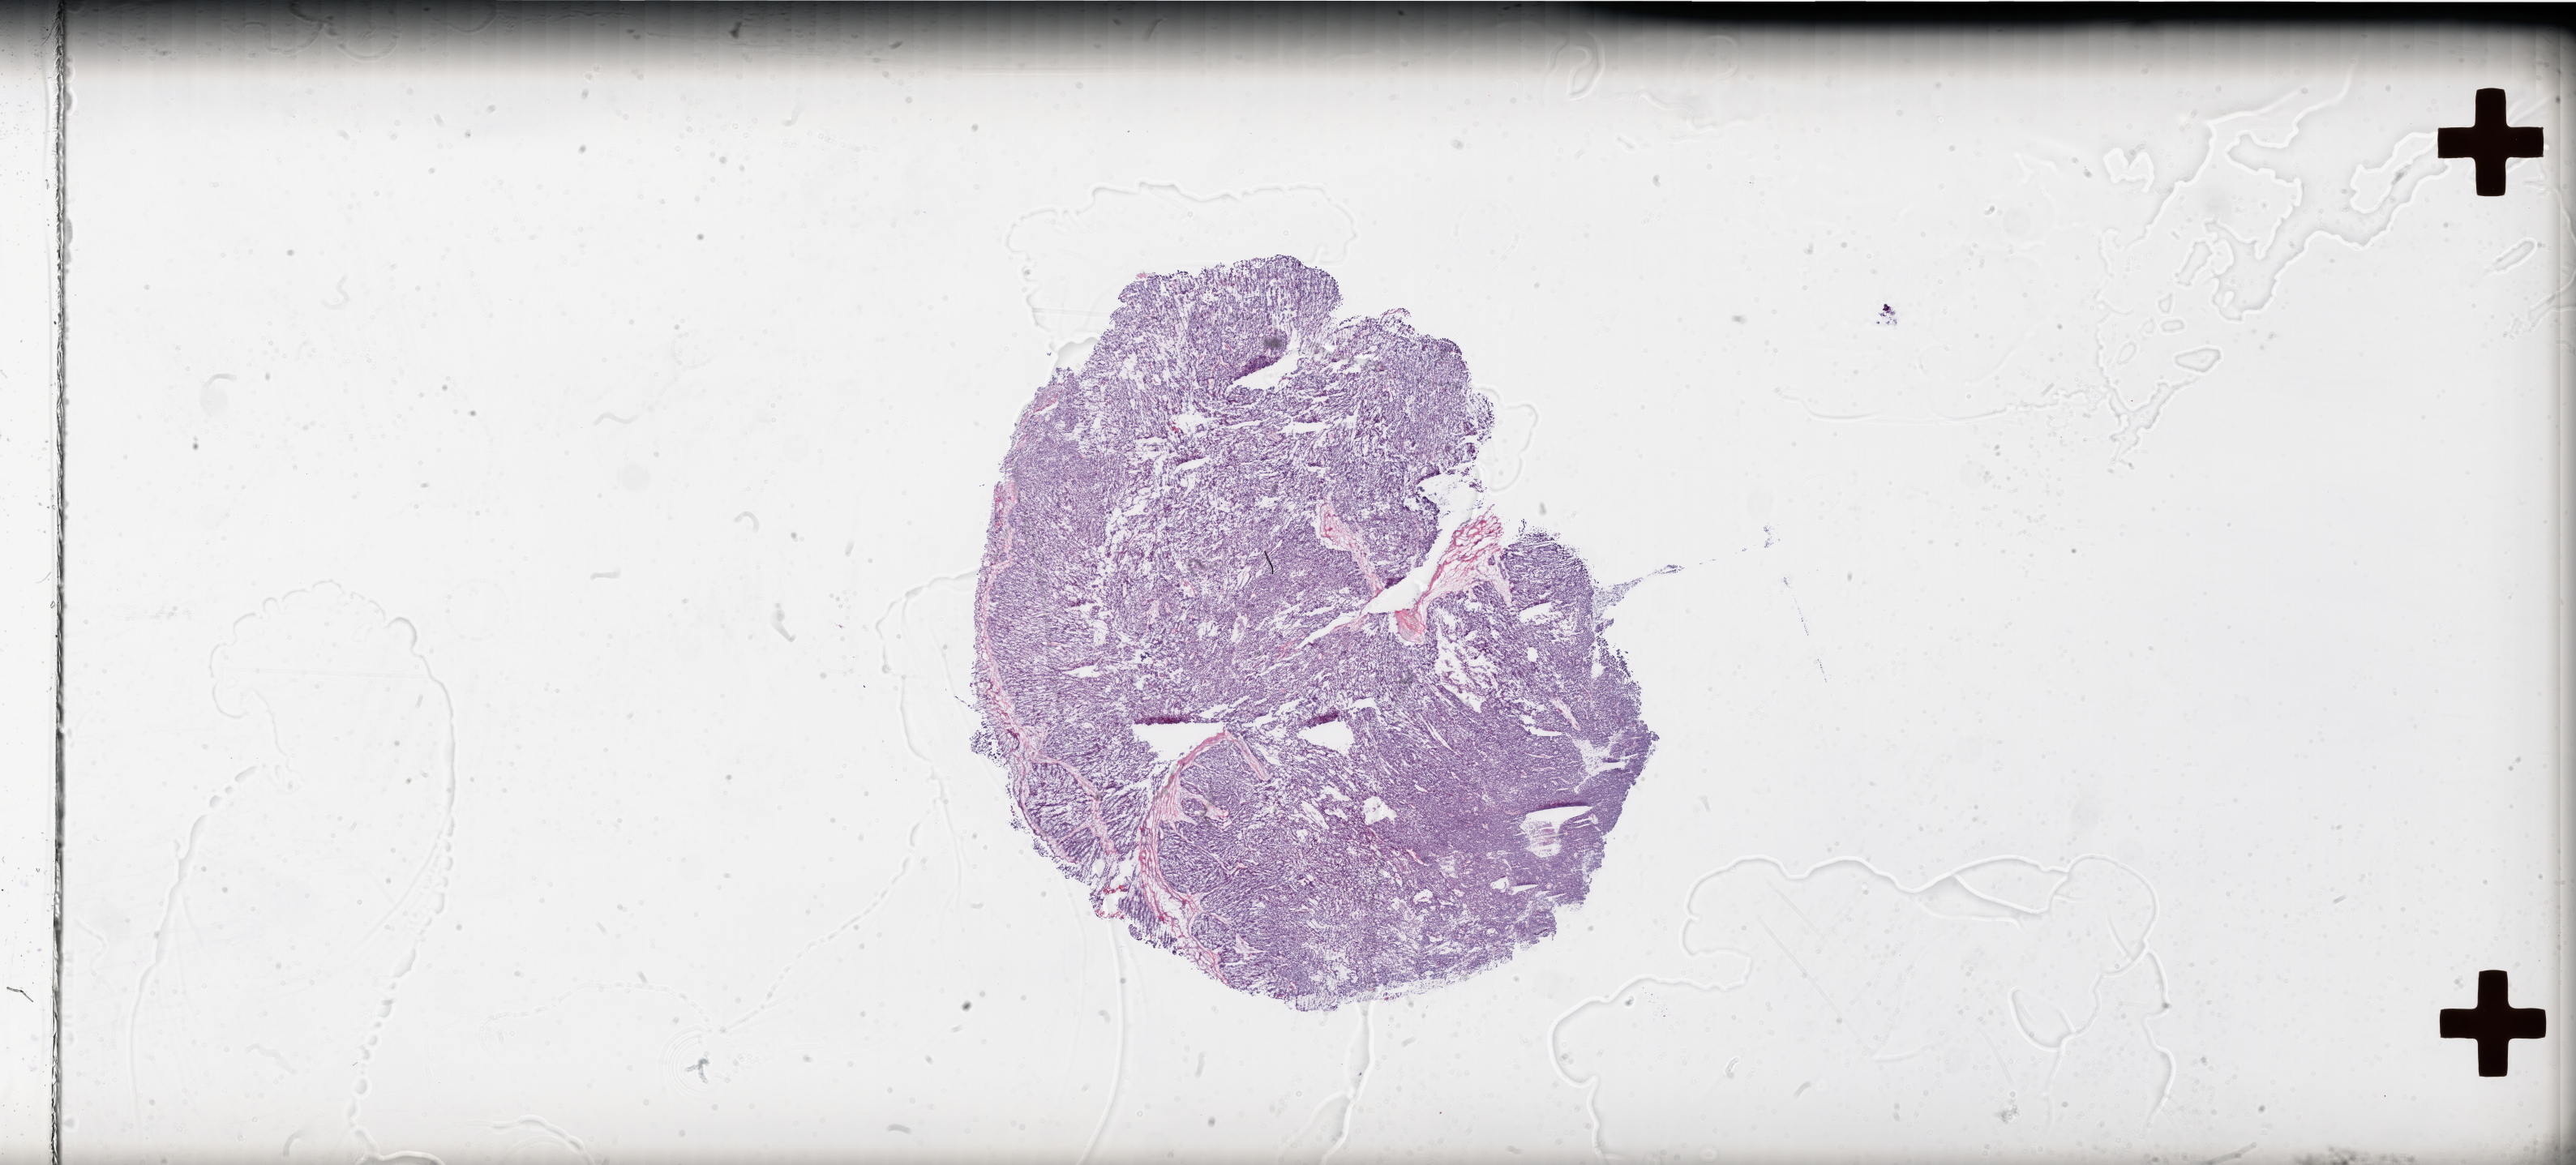
Whole-slide histology image, H&E, a low-resolution overview of the entire scanned area, about 51.1 x 23.1 mm (acquisition: 20x scan). Frozen section from the top of the tissue portion. Ovary, primary tumour sample. Female, age 73 years at initial diagnosis. Histologic grade: G3 (poorly differentiated). Composition of this section per pathologist review: tumour cells 95%, tumour nuclei 98%, normal cells 0%, stromal cells 5%, necrosis 0%.
Diagnosis: Serous cystadenocarcinoma, NOS. FIGO stage: IIIC.